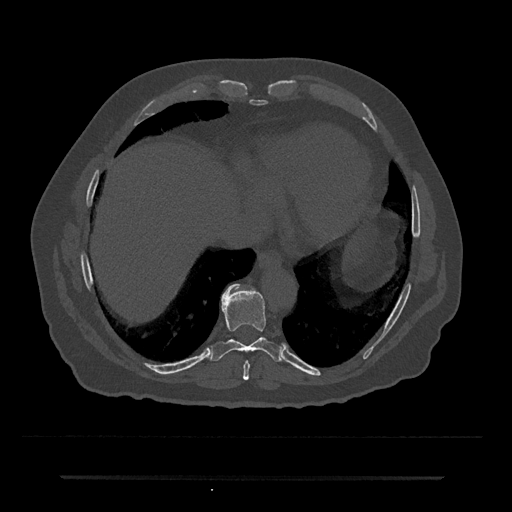
CT including the spine, one axial slice. Reconstruction kernel Br40s/3. Bone window (W 1800 / L 400 HU). 0.5 mm slice thickness. 512 × 512 image matrix, field of view 437 × 437 mm. Patient: male, 69 years. From the clinical record (not read from this slice): primary cancer: prostate.
Annotated regions visible in this slice (semi-automatic segmentation, software-assisted and operator-edited):
- T8 vertebra: bounding box (x1, y1, x2, y2) in pixels: (243, 361, 250, 380)
- T9 vertebra: (211, 284, 283, 362)